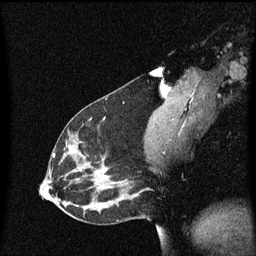
Breast MRI (dynamic contrast-enhanced), one sagittal slice; slice 30 of 60 in the series (ordered by position); dynamic contrast-enhanced series, image 2 of 3 at this slice position (ordered by acquisition); 1.5 T; TE 4.2 ms, TR 8.4 ms; 2 mm slice thickness; 256 × 256 image matrix, field of view 200 × 200 mm. Female patient, age 33 years.
Annotated regions visible in this slice (semi-automatic segmentation, software-assisted and operator-edited):
- analysis volume of interest (the breast-tissue region the enhancement analysis was run in; not a lesion): bounding box (x1, y1, x2, y2) in pixels: (45, 114, 152, 191)
- tumour enhancement mask (voxels above the 70 % enhancement threshold inside the analysis volume of interest): (54, 154, 110, 177)